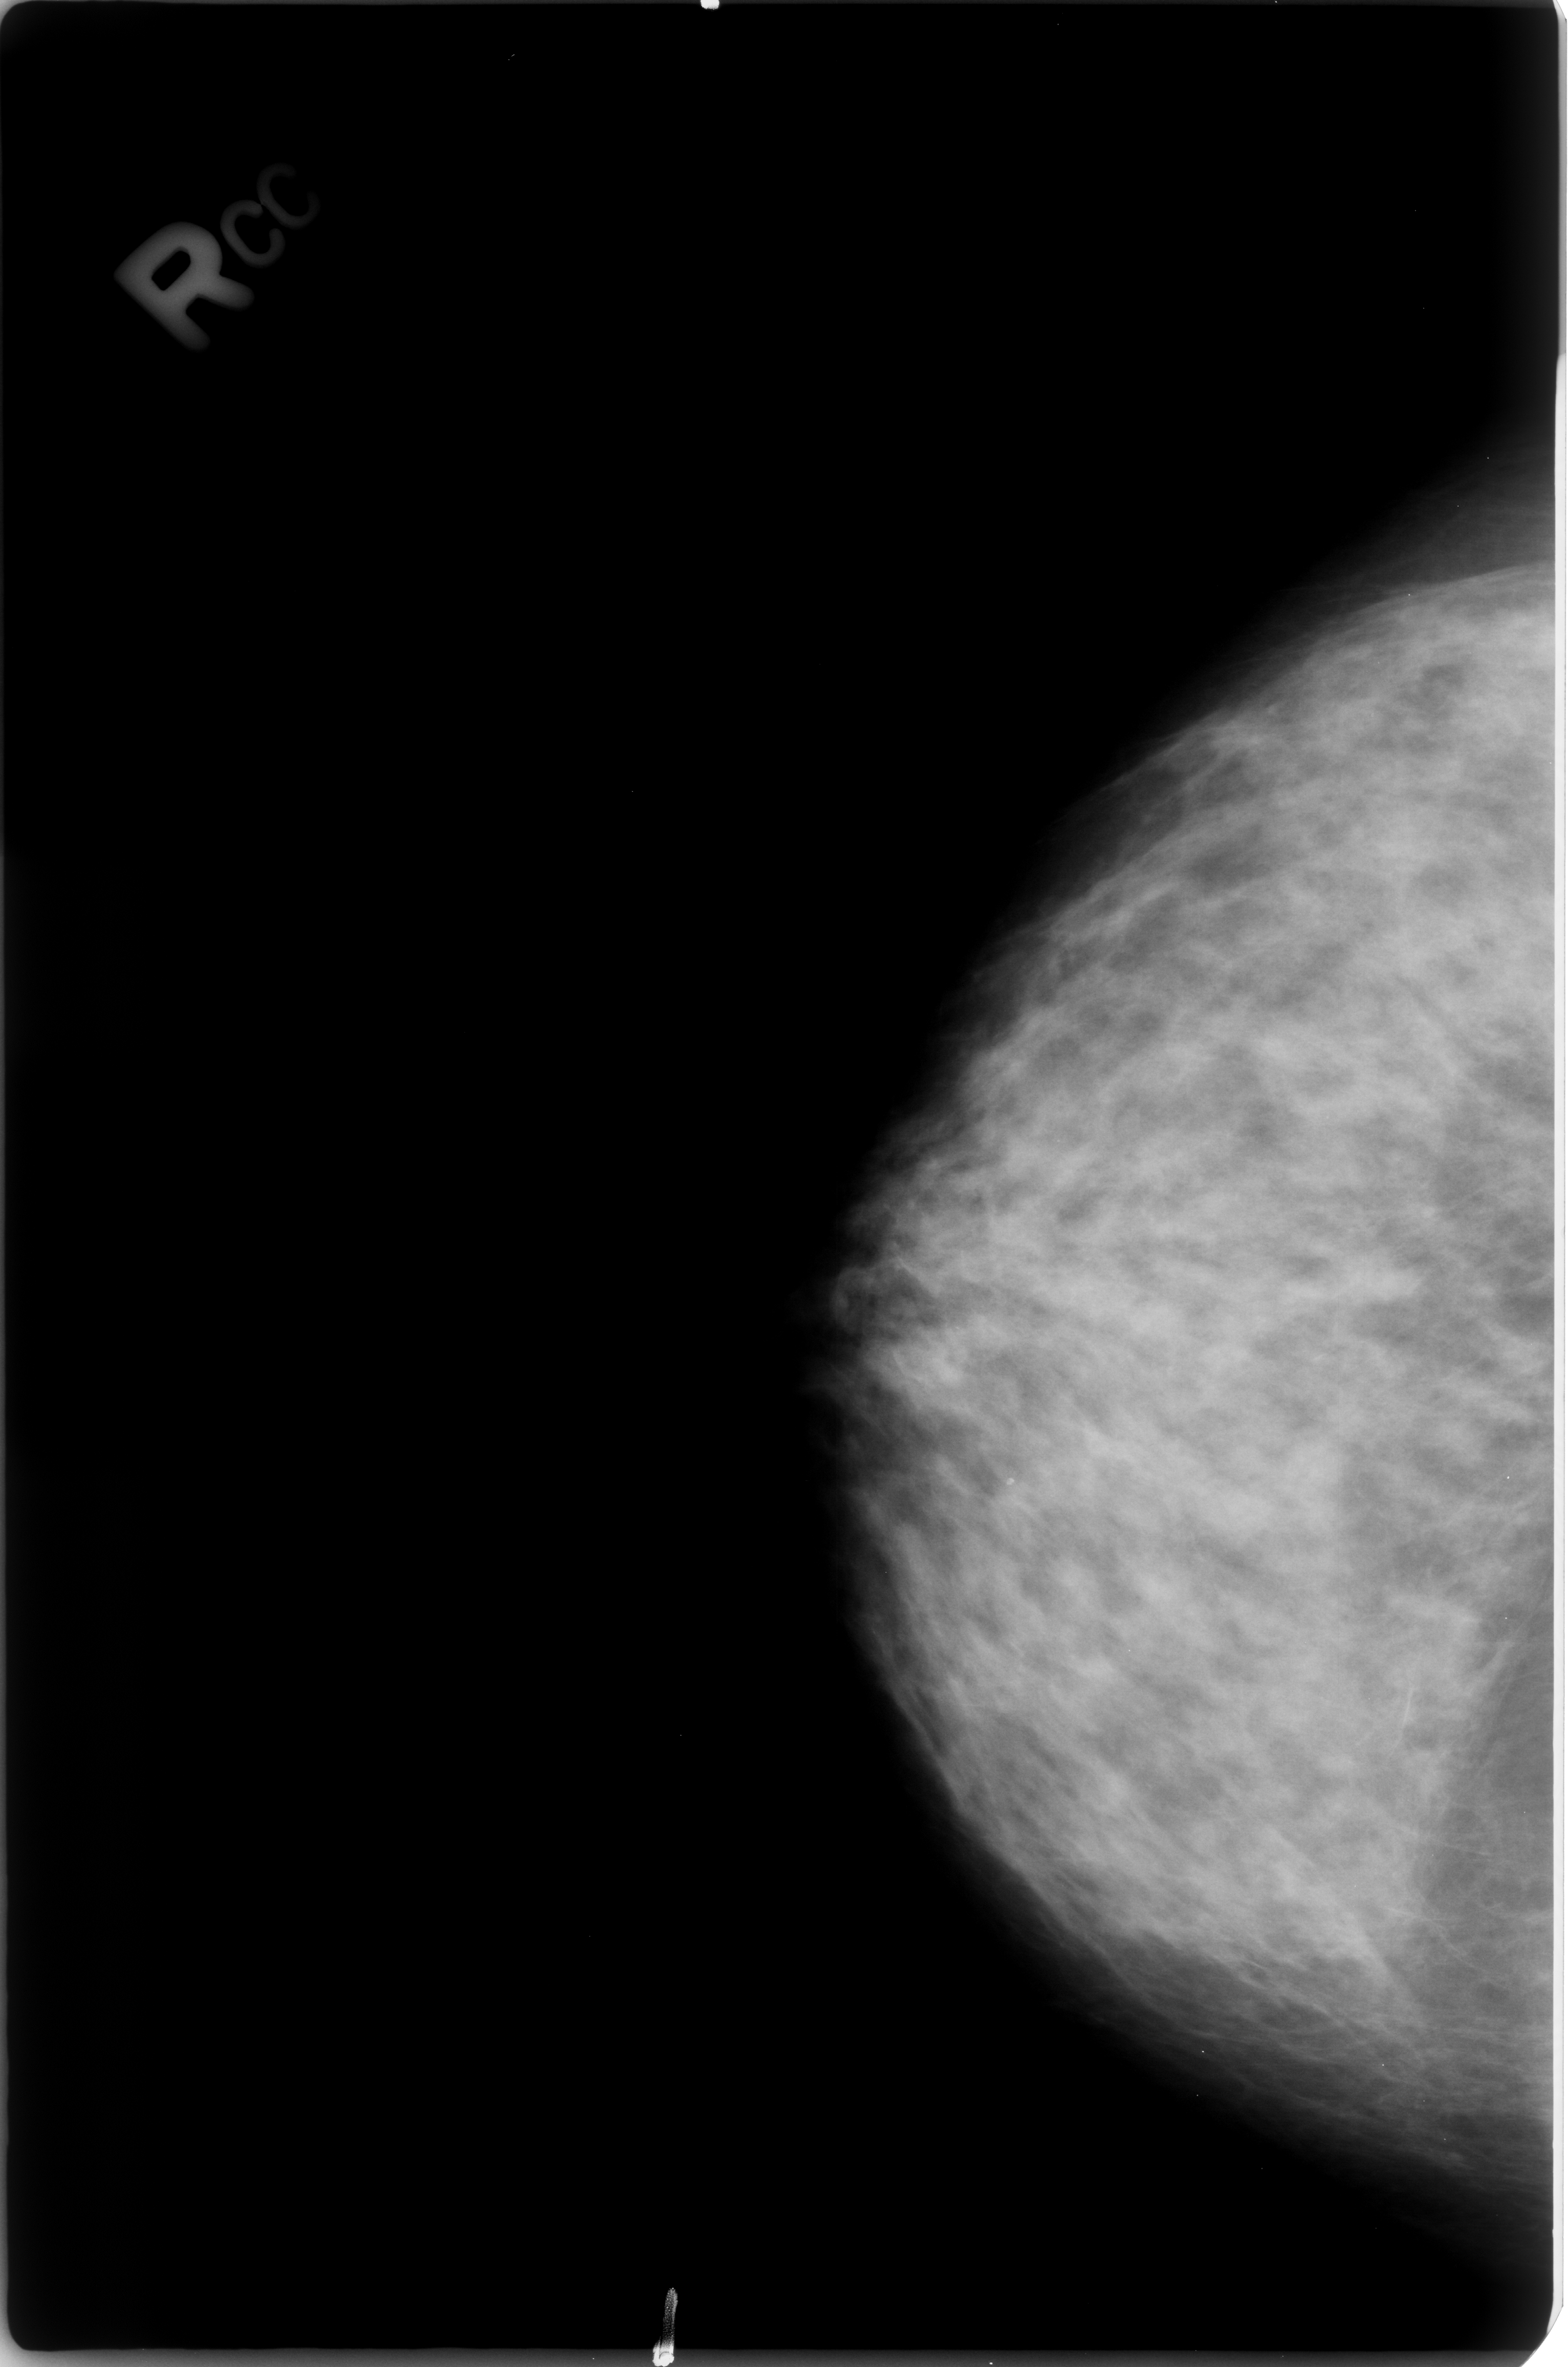
Scanned film-screen mammogram; right breast; craniocaudal (CC) view; breast composition: extremely dense (BI-RADS density category 4 of 4).
Abnormality record for this image: calcifications, morphology lucent center; BI-RADS assessment category 2; subtlety rating 3 on a 1 (subtle) to 5 (obvious) scale; benign without callback (not worked up further).